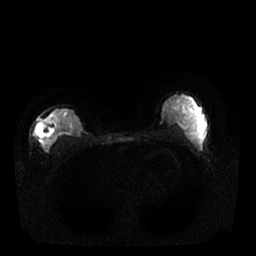
Breast MRI, one axial slice. Position 15 of 25 along the scan axis. Diffusion-weighted series; image 2 of 4 stored at this slice position (different b-values; order by instance number). 1.5 T. 256 × 256 image matrix, field of view 340 × 340 mm. Female patient.
Annotated regions visible in this slice (manually delineated by an expert):
- tumour on diffusion-weighted imaging: box from (x=35, y=123) to (x=54, y=151) px